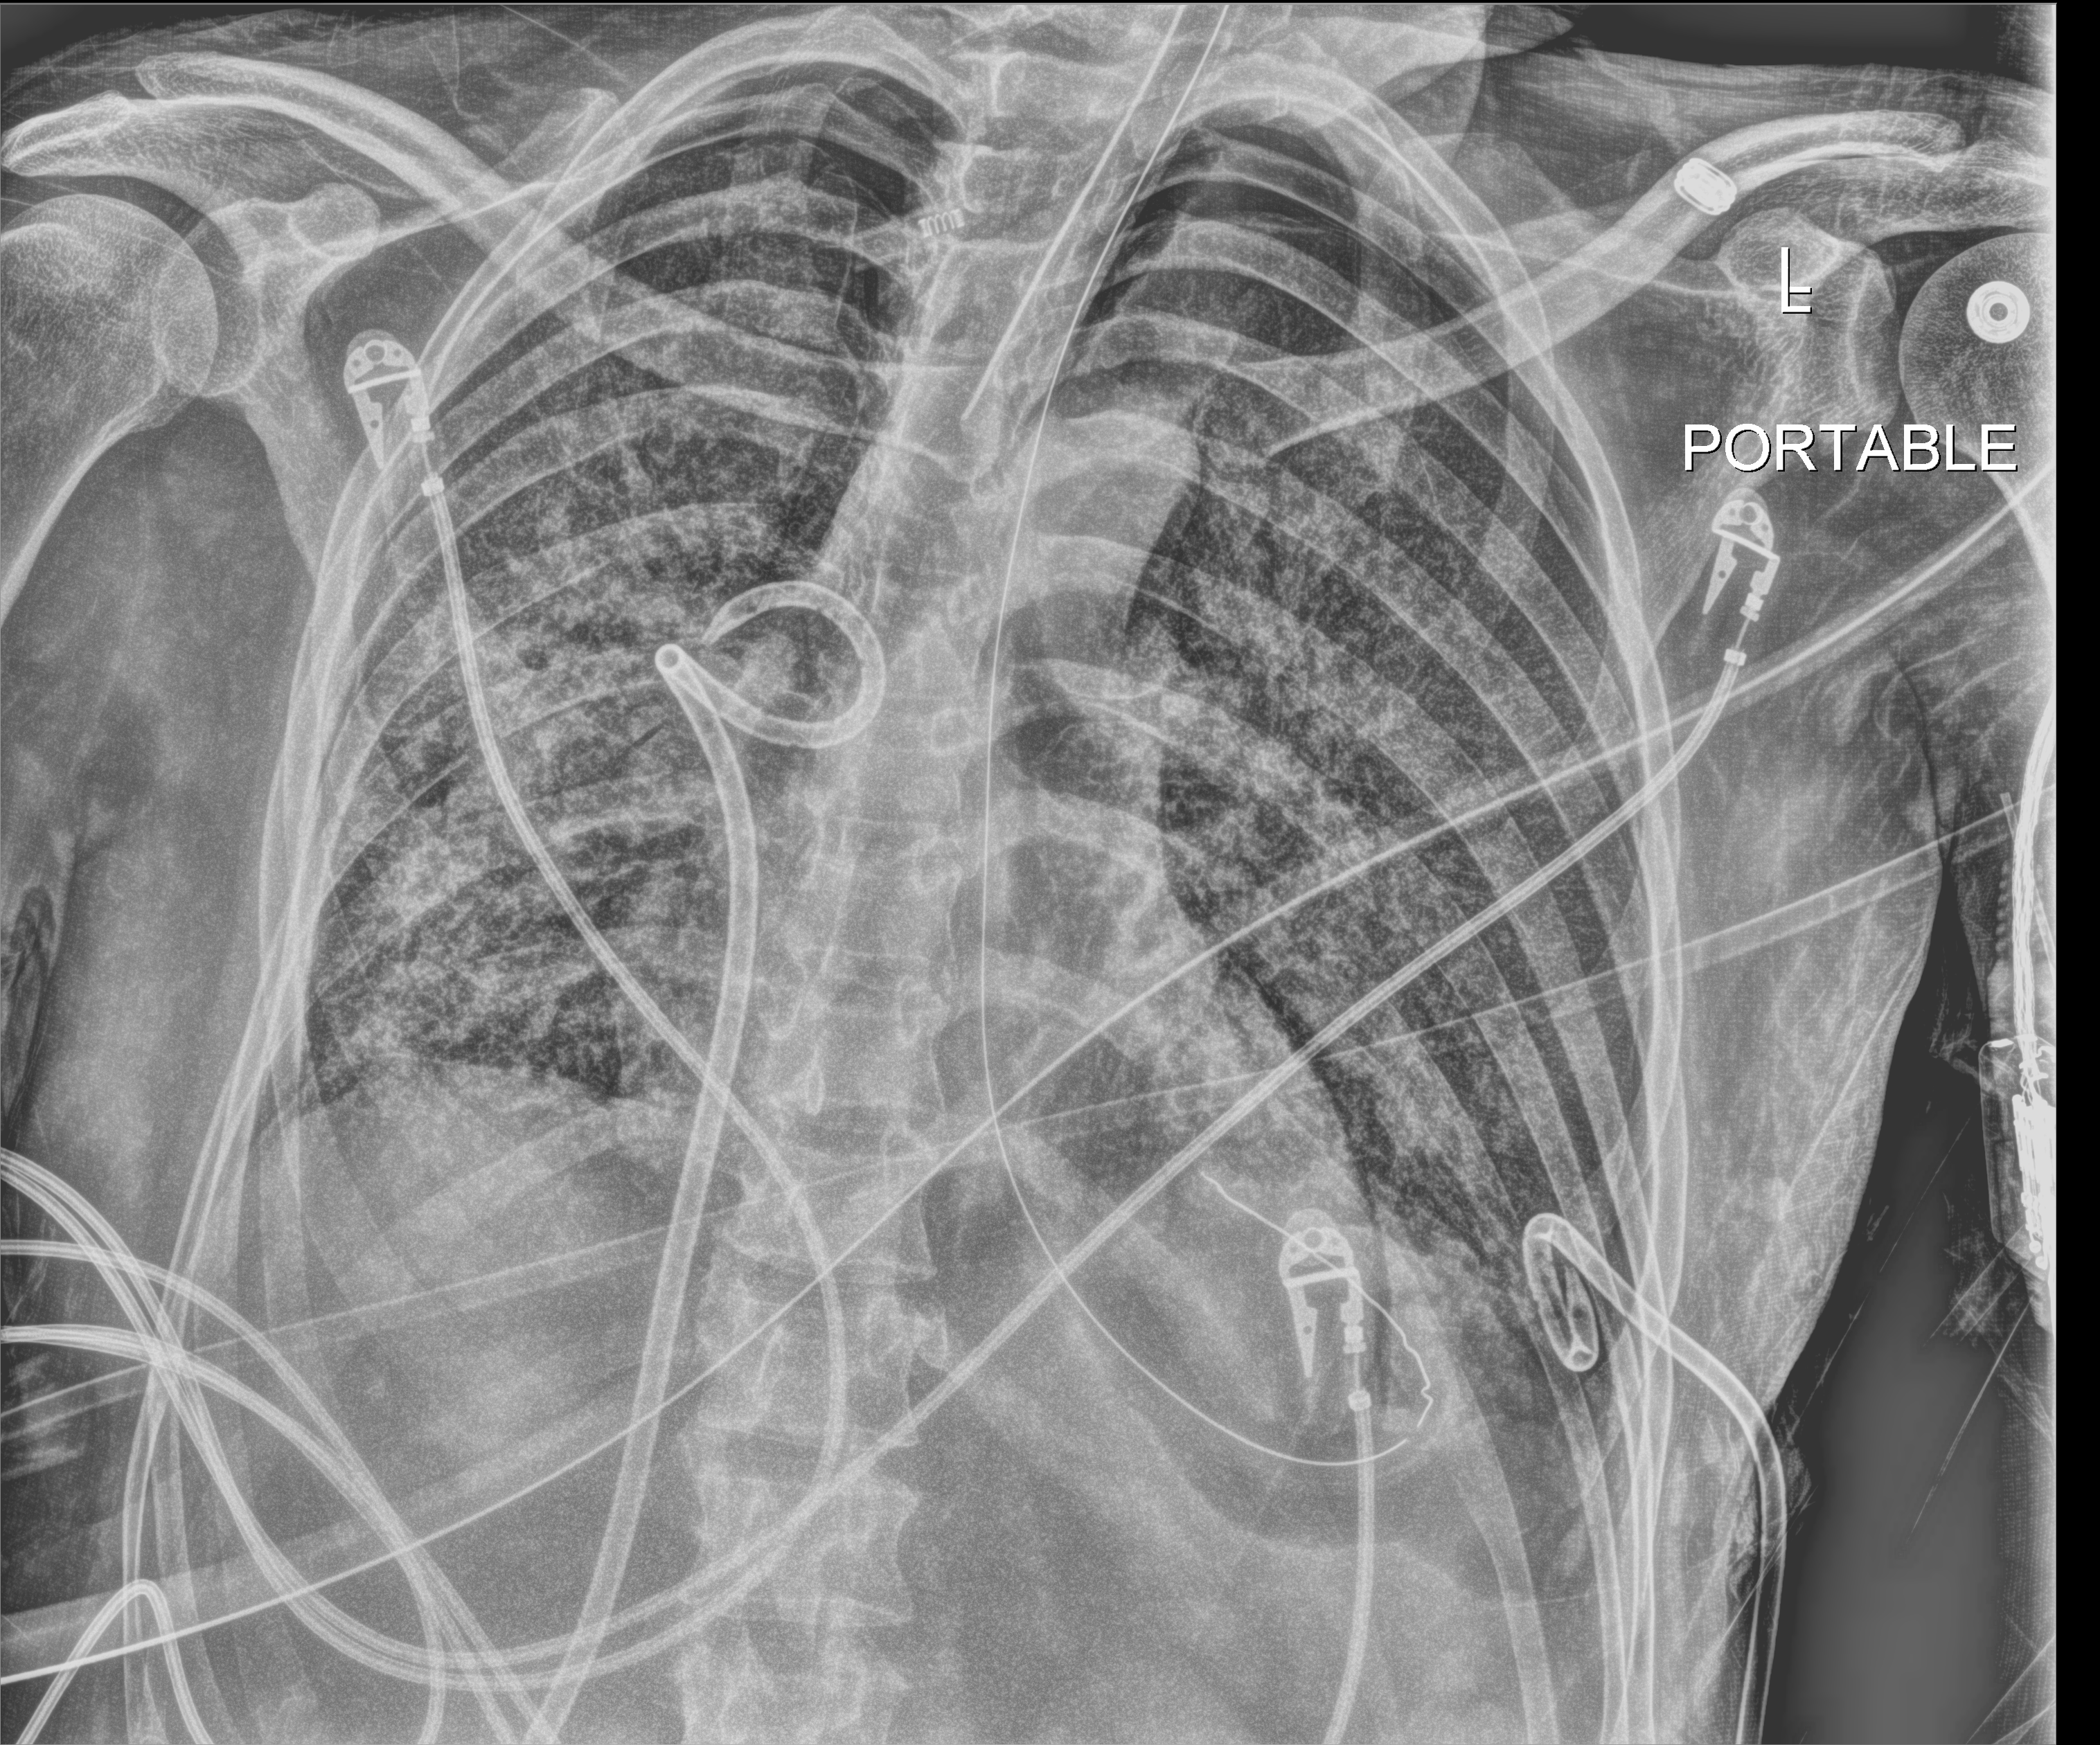
Bedside chest radiograph (digital radiography); anteroposterior (AP) projection. Adult patient hospitalised with COVID-19, age 18–59 years.
Admission-level facts for this patient (not findings on this image; timing relative to this image not recorded):
- COPD (admission record): no